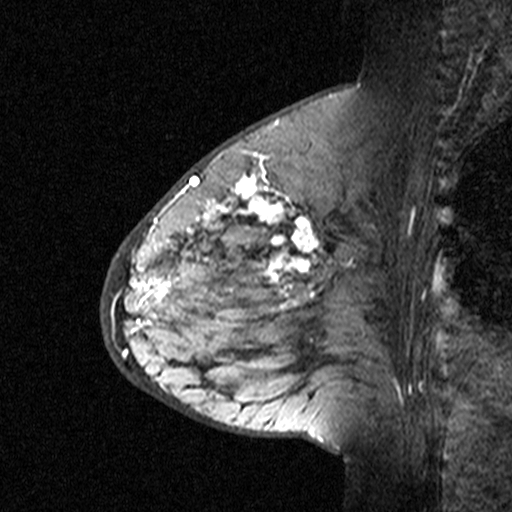
Breast MRI (dynamic contrast-enhanced), one sagittal slice. Slice 16 of 44 in the series (ordered by position). Dynamic contrast-enhanced study with each time point stored as its own series, time point 3 of 4 at this slice position (ordered by acquisition time). 1.5 T. TE 4.5 ms, TR 11 ms. 3 mm slice thickness. 512 × 512 image matrix. Patient: female, 65 years. Case-level facts recorded for this patient, not image findings: setting: breast cancer imaged before/during neoadjuvant chemotherapy; receptor status: HER2-positive.
Structures marked on this image (semi-automatically segmented with operator editing):
- analysis volume of interest (the breast-tissue region the enhancement analysis was run in; not a lesion): bounding box [x1, y1, x2, y2] px = [182, 190, 353, 361]
- tumour enhancement mask (voxels above the 90 % enhancement threshold inside the analysis volume of interest): [187, 190, 350, 312]